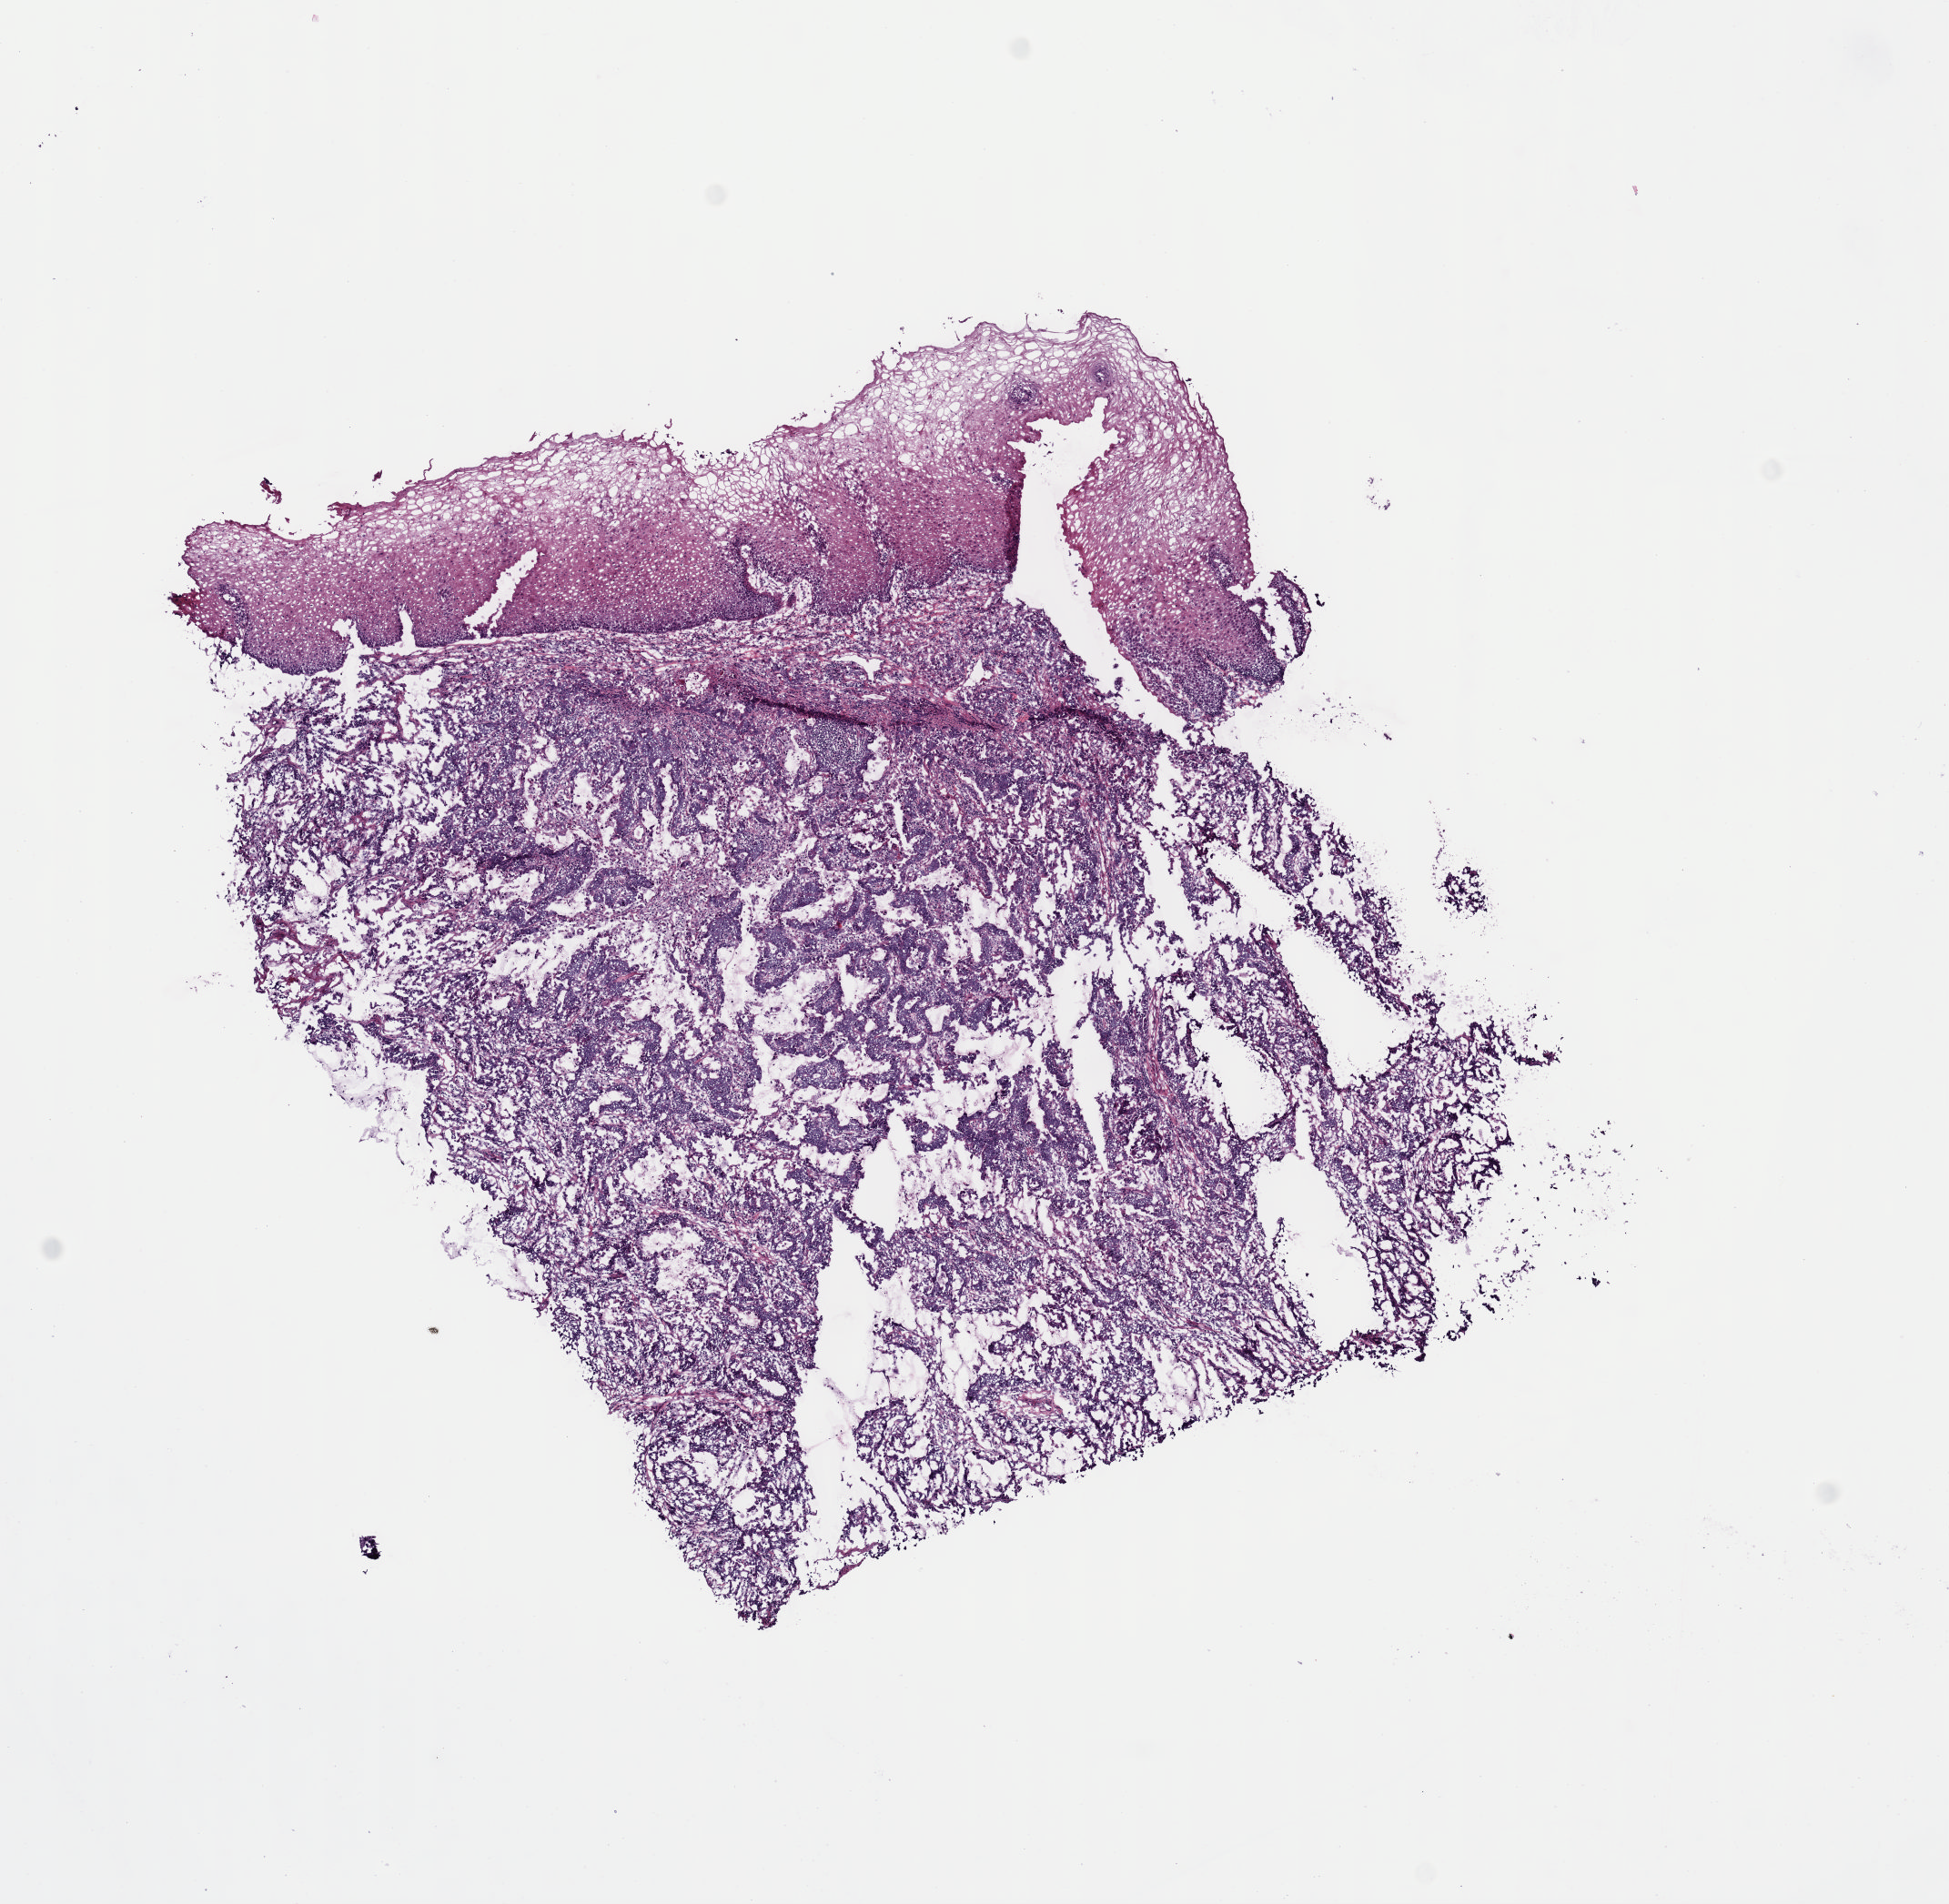
Hematoxylin and eosin (H&E) stained whole-slide image, whole scanned area (about 8.5 x 8.3 mm, from a 40x scan) shown as a low-resolution overview, frozen section from the top of the tissue portion, primary tumour sample from the esophagus. Male, age 81 years at initial diagnosis. Histologic grade: G2 (moderately differentiated). Slide review estimates, as recorded: tumour cells 70%, tumour nuclei 70%, normal cells 10%, stromal cells 20%, necrosis 0%. Inflammatory infiltration, as recorded: lymphocyte infiltration 7%, monocyte infiltration 0%, neutrophil infiltration 0%.
• AJCC pathologic stage: IIIB (7th edition)
• pathologic diagnosis: Adenocarcinoma, NOS (lower third of esophagus)